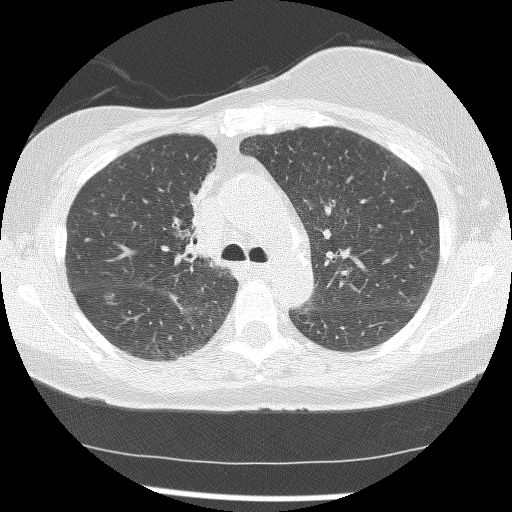
Axial slice from a low-dose chest CT screening exam, first (baseline) screen, lung window (W 1500 / L -600 HU), 2.5 mm slice thickness, slice 51 of 172 in the series, 512 × 512 image matrix, field of view 315 × 315 mm. Female participant, aged 56 years at enrolment.
Lesion marked by an expert reader, box from (x=163, y=167) to (x=219, y=264) px. The screening reader recorded 2 non-calcified nodules or masses ≥4 mm on this exam (right lower lobe, right middle lobe); which of them this box marks is not recorded. Official screen result: positive, change unspecified: nodule(s) >= 4 mm or enlarging nodule(s), mass(es), or other non-specific abnormalities suspicious for lung cancer. Participant outcome: lung cancer diagnosed 1185 days after this screen — adenocarcinoma, NOS, right upper lobe, stage IIIB (AJCC 6th edition), 8 mm at pathology.